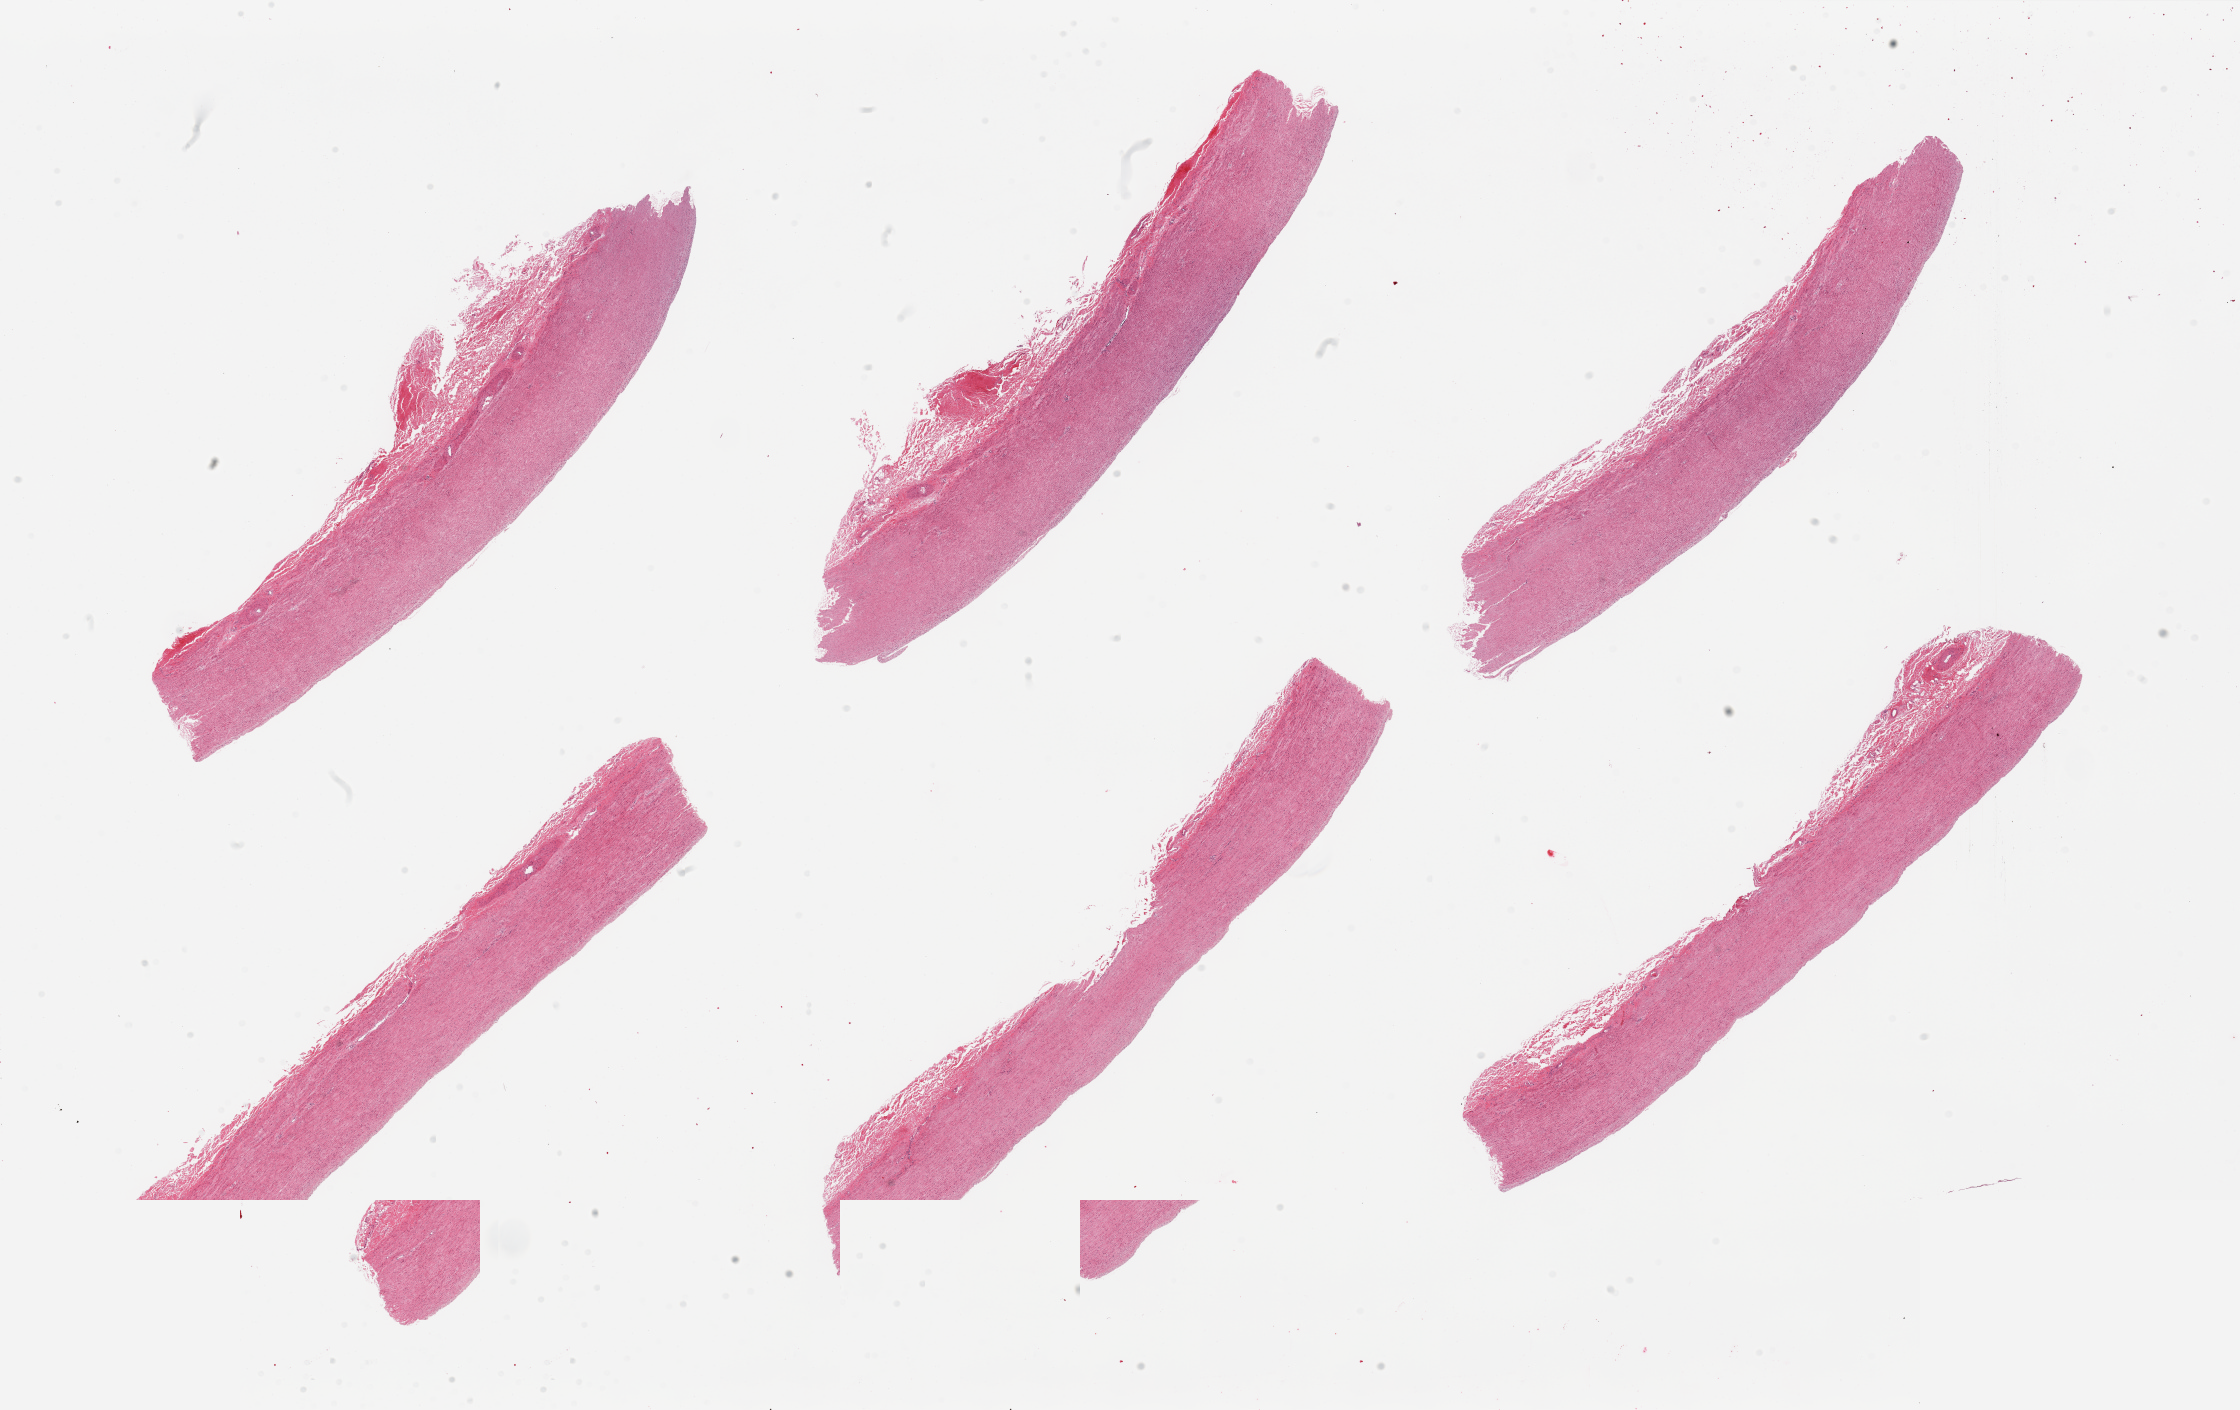
Whole-slide image, haematoxylin and eosin stain — low-resolution overview of the scanned area, about 35.4 x 22.3 mm, PAXgene-fixed paraffin-embedded (PFPE) section, sampled site (target tissue): aorta, donor tissue sample. Donor sex: male.
Pathologist's review note for this sample: 6 pieces.